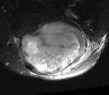
MRI of an extremity soft-tissue mass, one axial slice; slice 23 of 52 in the series (ordered by position); T2-weighted fat-saturated; MR volume resampled by the dataset authors to the PET/CT grid (not the native acquisition matrix); 3.27 mm slice thickness; 109 × 95 image matrix. Male patient. From the clinical record (not read from this slice): histological type: synovial sarcoma; site of the primary tumour: left poplietal fossa.
Outlined on this slice (expert contour drawn on MRI and transferred to this co-registered scan by the dataset authors):
- gross tumour volume (mass): bounding box <17,17,89,75> (left, top, right, bottom; pixels)